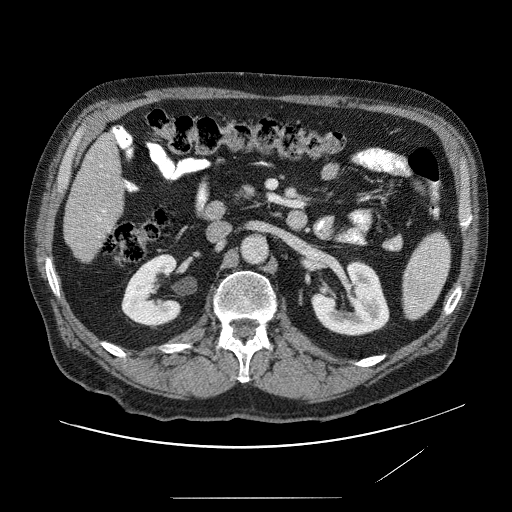
Contrast-enhanced abdominal CT (liver protocol), one axial slice. Position 17 of 89 along the scan axis. Reconstruction kernel STANDARD. Soft-tissue window (W 400 / L 40 HU). 2.5 mm slice thickness. 512 × 512 image matrix, field of view 420 × 420 mm. Case-level facts recorded for this patient, not image findings: diagnosis: hepatocellular carcinoma (patient treated with transarterial chemoembolisation; whether this scan precedes or follows treatment is not stated here); TNM stage (as recorded): Stage-IVA; Child-Pugh class: A; tumour differentiation: moderately differentiated; tumour nodularity: multinodular.
Outlined on this slice (semi-automatic segmentation, software-assisted and operator-edited):
- liver parenchyma outside the tumour (the mass and vessels are separate outlines, so this box may not span the whole liver): bounding box <62,127,132,266> (left, top, right, bottom; pixels)
- liver vessels: <102,169,119,219>